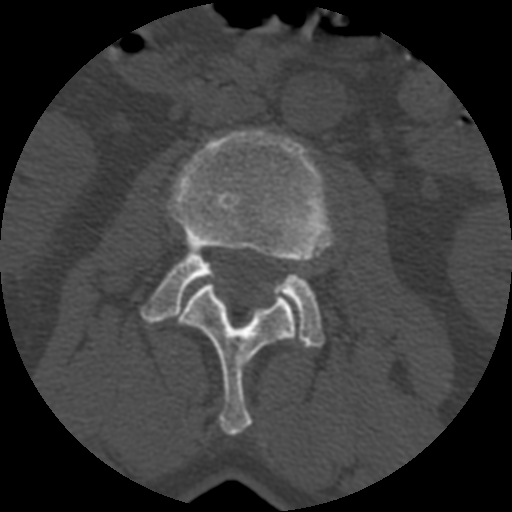
CT including the spine, one axial slice; position 320 of 399 along the scan axis; reconstruction kernel STANDARD; 120 kVp; bone window (W 1800 / L 400 HU); 1.25 mm slice thickness; 512 × 512 image matrix, field of view 160 × 160 mm. Patient age 71 years. Case-level facts recorded for this patient, not image findings: primary cancer: prostate.
Structures marked on this image (semi-automatically segmented with operator editing):
- L2 vertebra: bounding box (x1, y1, x2, y2) in pixels: (173, 282, 295, 436)
- L3 vertebra: (141, 129, 338, 348)